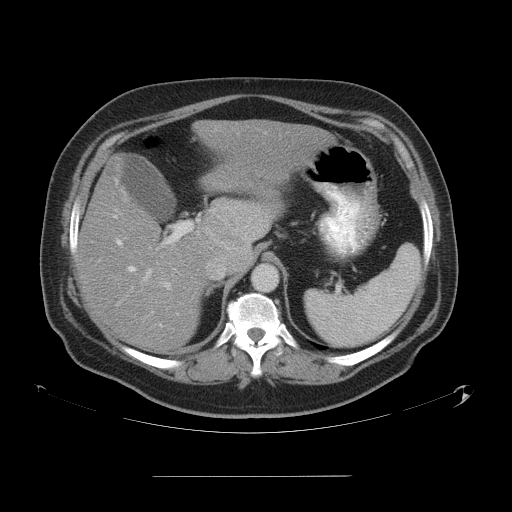
Contrast-enhanced abdominal CT, one axial slice. Slice 36 of 58 in the series (ordered by position). 120 kVp. Soft-tissue window (W 400 / L 40 HU). 5 mm slice thickness. 512 × 512 image matrix, field of view 480 × 480 mm. Male patient, age 63 years. From the clinical record (not read from this slice): diagnosis: colorectal cancer liver metastases, imaged before liver resection; multiple liver metastases: no; largest metastasis: 4.2 cm; disease in both lobes: no.
Annotated regions visible in this slice (manually delineated by an expert):
- hepatic veins: bounding box (x1, y1, x2, y2) in pixels: (113, 210, 224, 270)
- liver: (80, 120, 326, 351)
- planned liver remnant (the part of the liver to remain after resection): (80, 193, 206, 351)
- portal vein (with intrahepatic branches): (117, 222, 192, 327)
- liver metastasis: (216, 224, 243, 249)